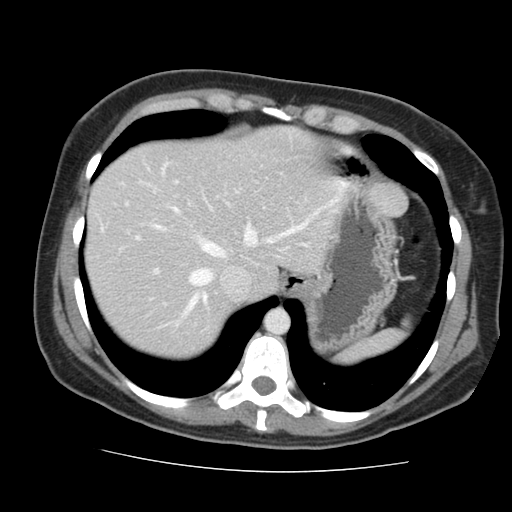
Contrast-enhanced abdominal CT, one axial slice; slice 123 of 144 in the series (ordered by position); 120 kVp; intravenous contrast given; soft-tissue window (W 400 / L 40 HU); 2.5 mm slice thickness; 512 × 512 image matrix, field of view 333 × 333 mm. Female patient, age 46 years. From the clinical record (not read from this slice): diagnosis: colorectal cancer liver metastases, imaged before liver resection; multiple liver metastases: no; largest metastasis: 2.8 cm; disease in both lobes: no.
Outlined on this slice (manually delineated by an expert):
- hepatic veins: box from (x=154, y=193) to (x=344, y=317) px
- liver: (x=87, y=128)–(x=338, y=360)
- planned liver remnant (the part of the liver to remain after resection): (x=87, y=128)–(x=338, y=360)
- portal vein (with intrahepatic branches): (x=136, y=237)–(x=157, y=273)